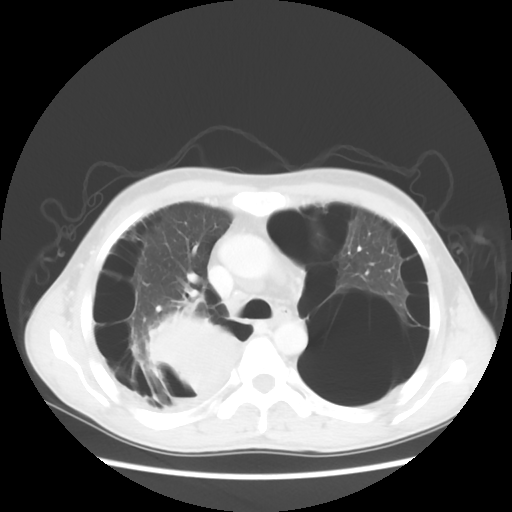
Chest CT, one axial slice. Slice 37 of 56 in the series (ordered by position). Reconstruction kernel STANDARD. 140 kVp. Lung window (W 1500 / L -600 HU). 512 × 512 image matrix, field of view 351 × 351 mm. Male patient, age 41 years. Case-level facts recorded for this patient, not image findings: clinical TNM (as recorded): T4 N0 M1a.
Structures marked on this image (bounding box drawn by a radiologist):
- lung tumour (recorded histology: large cell carcinoma): bounding box <148,312,244,406> (left, top, right, bottom; pixels)